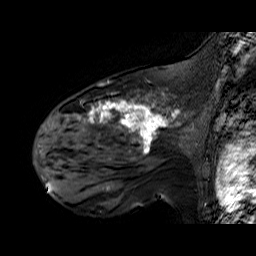
Breast MRI (dynamic contrast-enhanced), one sagittal slice; position 41 of 60 along the scan axis; dynamic contrast-enhanced series, time point 2 of 6 at this slice position (early post-contrast); 1.5 T; TE 6.3 ms, TR 32.9 ms; 256 × 256 image matrix, field of view 200 × 200 mm. Female patient. Case-level facts recorded for this patient, not image findings: setting: breast cancer imaged before/during neoadjuvant chemotherapy; receptor status: HER2-positive.
Outlined on this slice (semi-automatic segmentation, software-assisted and operator-edited):
- analysis volume of interest (the breast-tissue region the enhancement analysis was run in; not a lesion): bounding box <48,92,195,174> (left, top, right, bottom; pixels)
- tumour enhancement mask (voxels above the 100 % enhancement threshold inside the analysis volume of interest): <77,93,168,152>